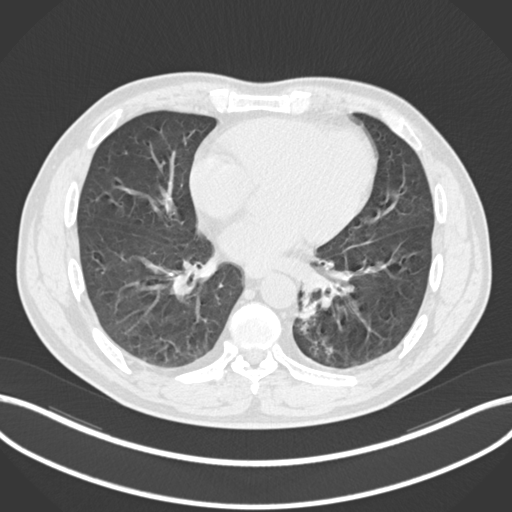
Chest CT, one axial slice. Position 86 of 223 along the scan axis. Lung window (W 1500 / L -600 HU). 512 × 512 image matrix, field of view 400 × 400 mm. Male patient, age 50 years. From the clinical record (not read from this slice): clinical TNM (as recorded): T2a N3 M0.
Annotated regions visible in this slice (rectangle marked by the reading radiologist):
- lung tumour (recorded histology: squamous cell carcinoma): box from (x=292, y=289) to (x=319, y=326) px